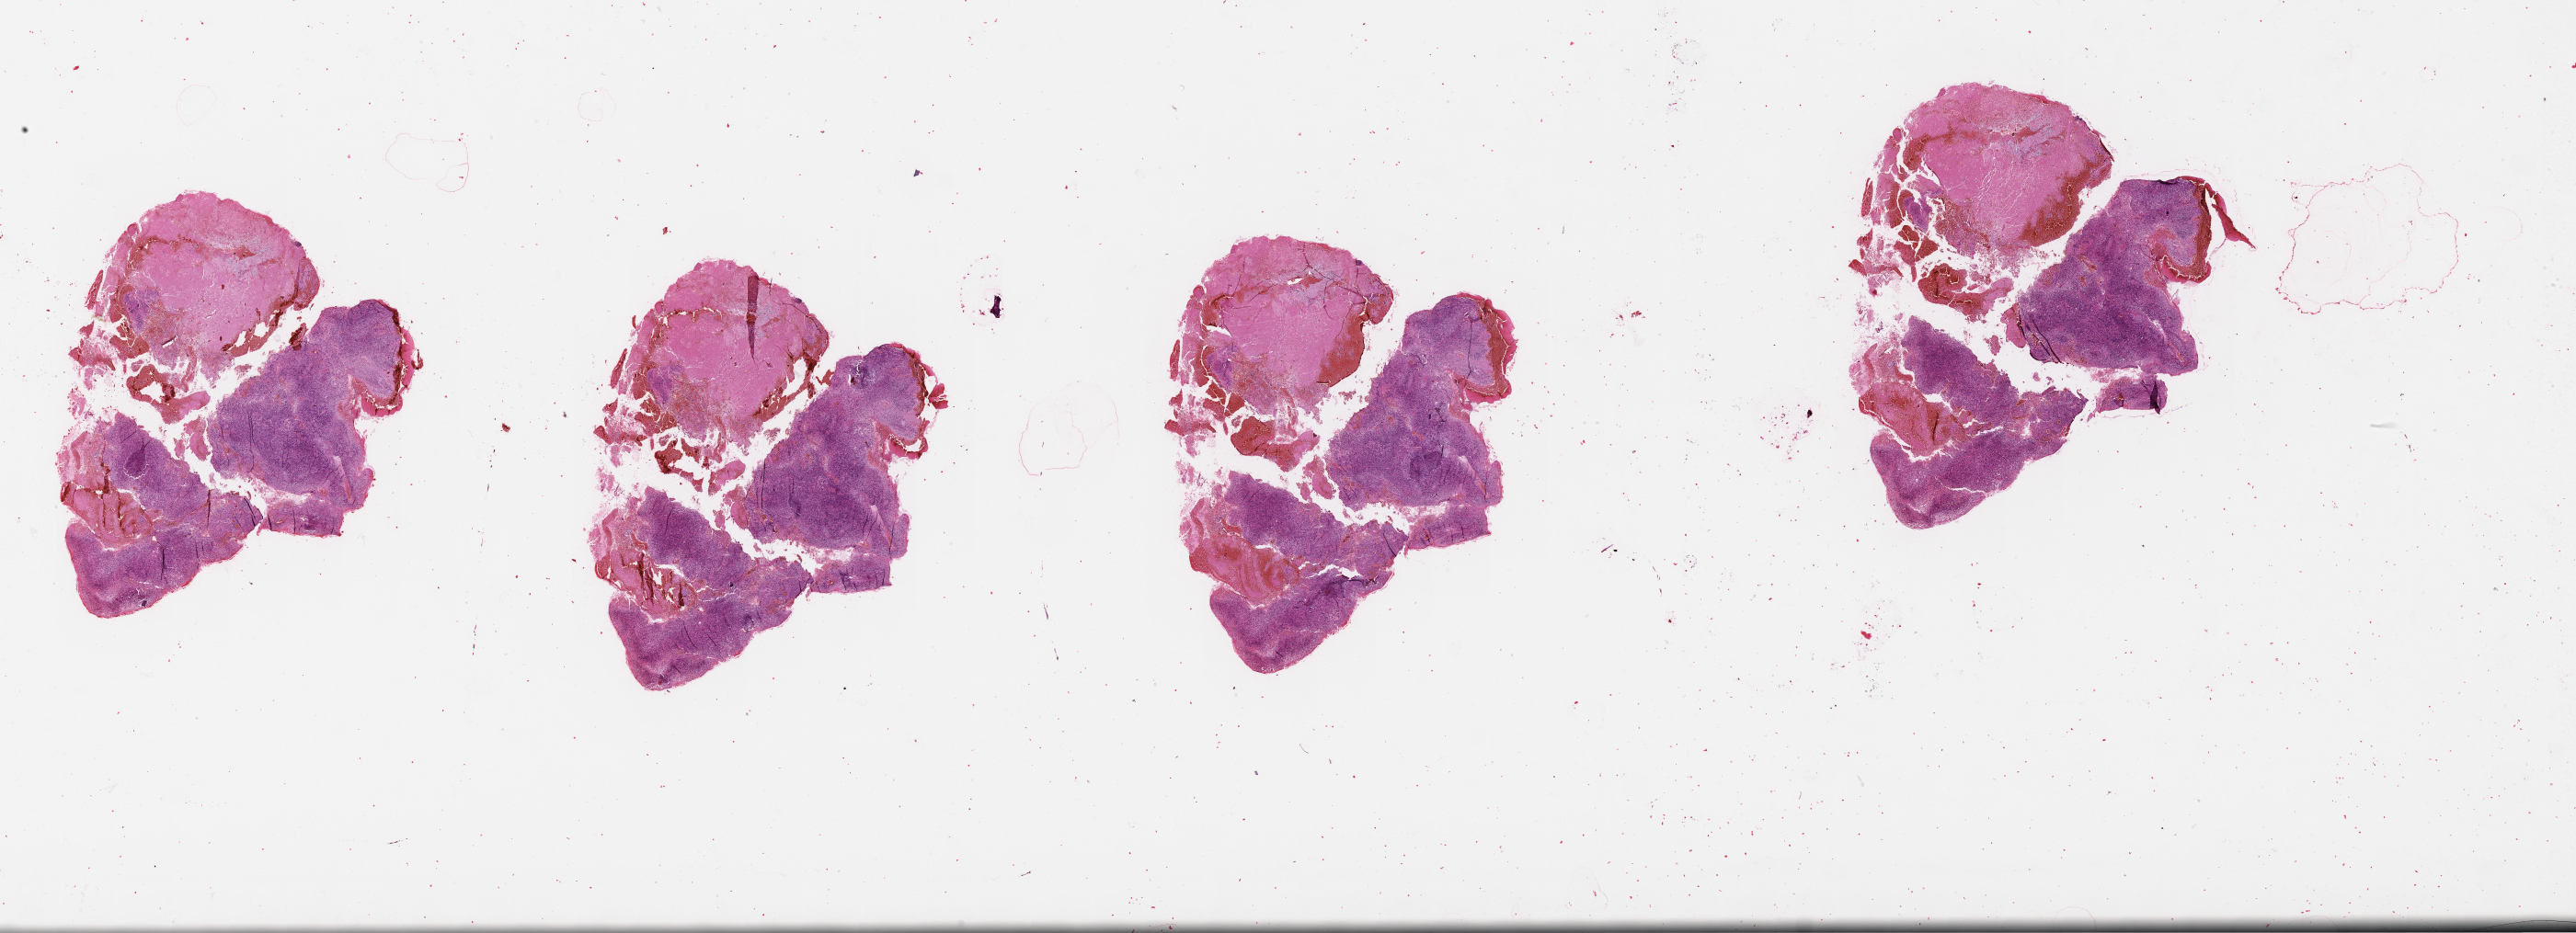
Digitized H&E-stained tissue section (whole slide) — whole scanned area (about 45.1 x 16.3 mm, from a 20x scan) shown as a low-resolution overview. Brain, tumour tissue. 37-year-old female patient.
Primary tumour site (as recorded): occipital lobe. Diagnosis: Glioblastoma.